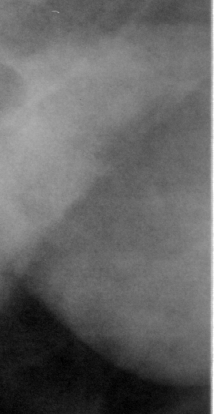
Region of interest cut from a scanned film mammogram (one marked finding), right breast, CC view, BI-RADS breast density category 3 (scale 1–4).
Mass, shape round, margins circumscribed; BI-RADS assessment category 3; pathology result (as recorded, not read from the image): benign.